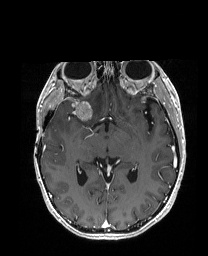
Brain MRI from a brain-tumour surgery series, one axial slice. Position 101 of 192 along the scan axis. T1-weighted post-contrast. 208 × 256 image matrix, field of view 203 × 250 mm. Case-level facts recorded for this patient, not image findings: histopathology: Metastatic Carcinoma from Breast primary; tumour location: Right Frontal.
Structures marked on this image (manually delineated by an expert):
- tumour: bounding box (x1, y1, x2, y2) in pixels: (55, 98, 104, 119)